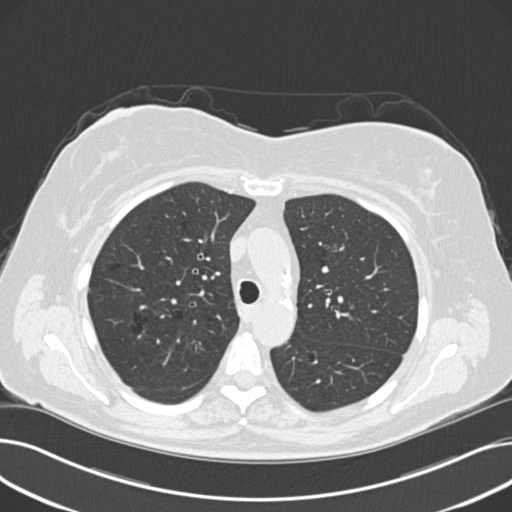
Low-dose screening chest CT, axial slice. Third annual screen. Lung window (W 1500 / L -600 HU). Standard (soft-tissue) reconstruction kernel (B30f). Female, age 60 years at enrolment. Current smoker at enrolment.
Expert-annotated lung lesion, bounding box (x1, y1, x2, y2) in pixels: (310, 229, 364, 271). The screening reader recorded 8 non-calcified nodules or masses ≥4 mm on this exam (right upper lobe, lingula, lingula, right middle lobe, right lower lobe, left lower lobe, left lower lobe, left lower lobe); which of them this box marks is not recorded. Official screen result: positive, other. Participant outcome: lung cancer diagnosed 176 days after this screen — non-small cell carcinoma, left upper lobe, poorly differentiated (G3), stage IB (AJCC 6th edition), 7 mm at pathology.